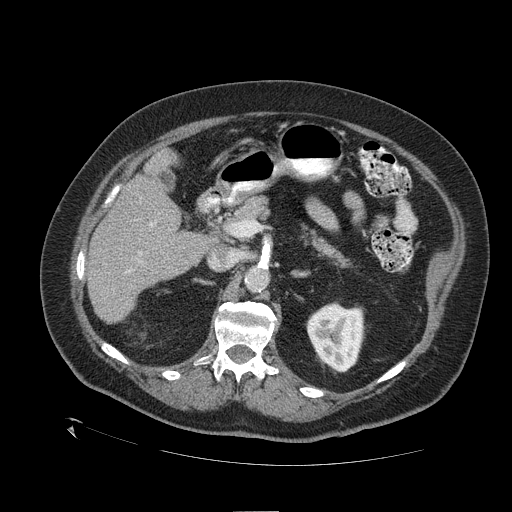
Contrast-enhanced abdominal CT (liver protocol), one axial slice. Slice 60 of 109 in the series (ordered by position). Reconstruction kernel STANDARD. 120 kVp. One of 2 acquisitions stored at this slice position. Soft-tissue window (W 400 / L 40 HU). 2.5 mm slice thickness. 512 × 512 image matrix. From the clinical record (not read from this slice): diagnosis: hepatocellular carcinoma (patient treated with transarterial chemoembolisation; whether this scan precedes or follows treatment is not stated here); TNM stage (as recorded): Stage-I; Child-Pugh class: A; tumour differentiation: no biopsy; tumour nodularity: uninodular.
Outlined on this slice (semi-automatic segmentation, software-assisted and operator-edited):
- liver parenchyma outside the tumour (the mass and vessels are separate outlines, so this box may not span the whole liver): bounding box (x1, y1, x2, y2) in pixels: (88, 168, 208, 322)
- liver vessels: (139, 223, 153, 262)